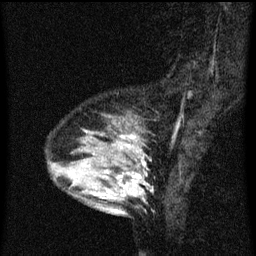
Breast MRI (dynamic contrast-enhanced), one sagittal slice. Position 17 of 60 along the scan axis. Dynamic contrast-enhanced series, image 2 of 3 at this slice position (ordered by acquisition). 1.5 T. TE 4.2 ms, TR 8 ms. 2 mm slice thickness. 256 × 256 image matrix, field of view 180 × 180 mm. Patient: female, 33 years.
Outlined on this slice (semi-automatically segmented with operator editing):
- analysis volume of interest (the breast-tissue region the enhancement analysis was run in; not a lesion): bounding box <61,126,146,213> (left, top, right, bottom; pixels)
- tumour enhancement mask (voxels above the 70 % enhancement threshold inside the analysis volume of interest): <119,136,143,197>